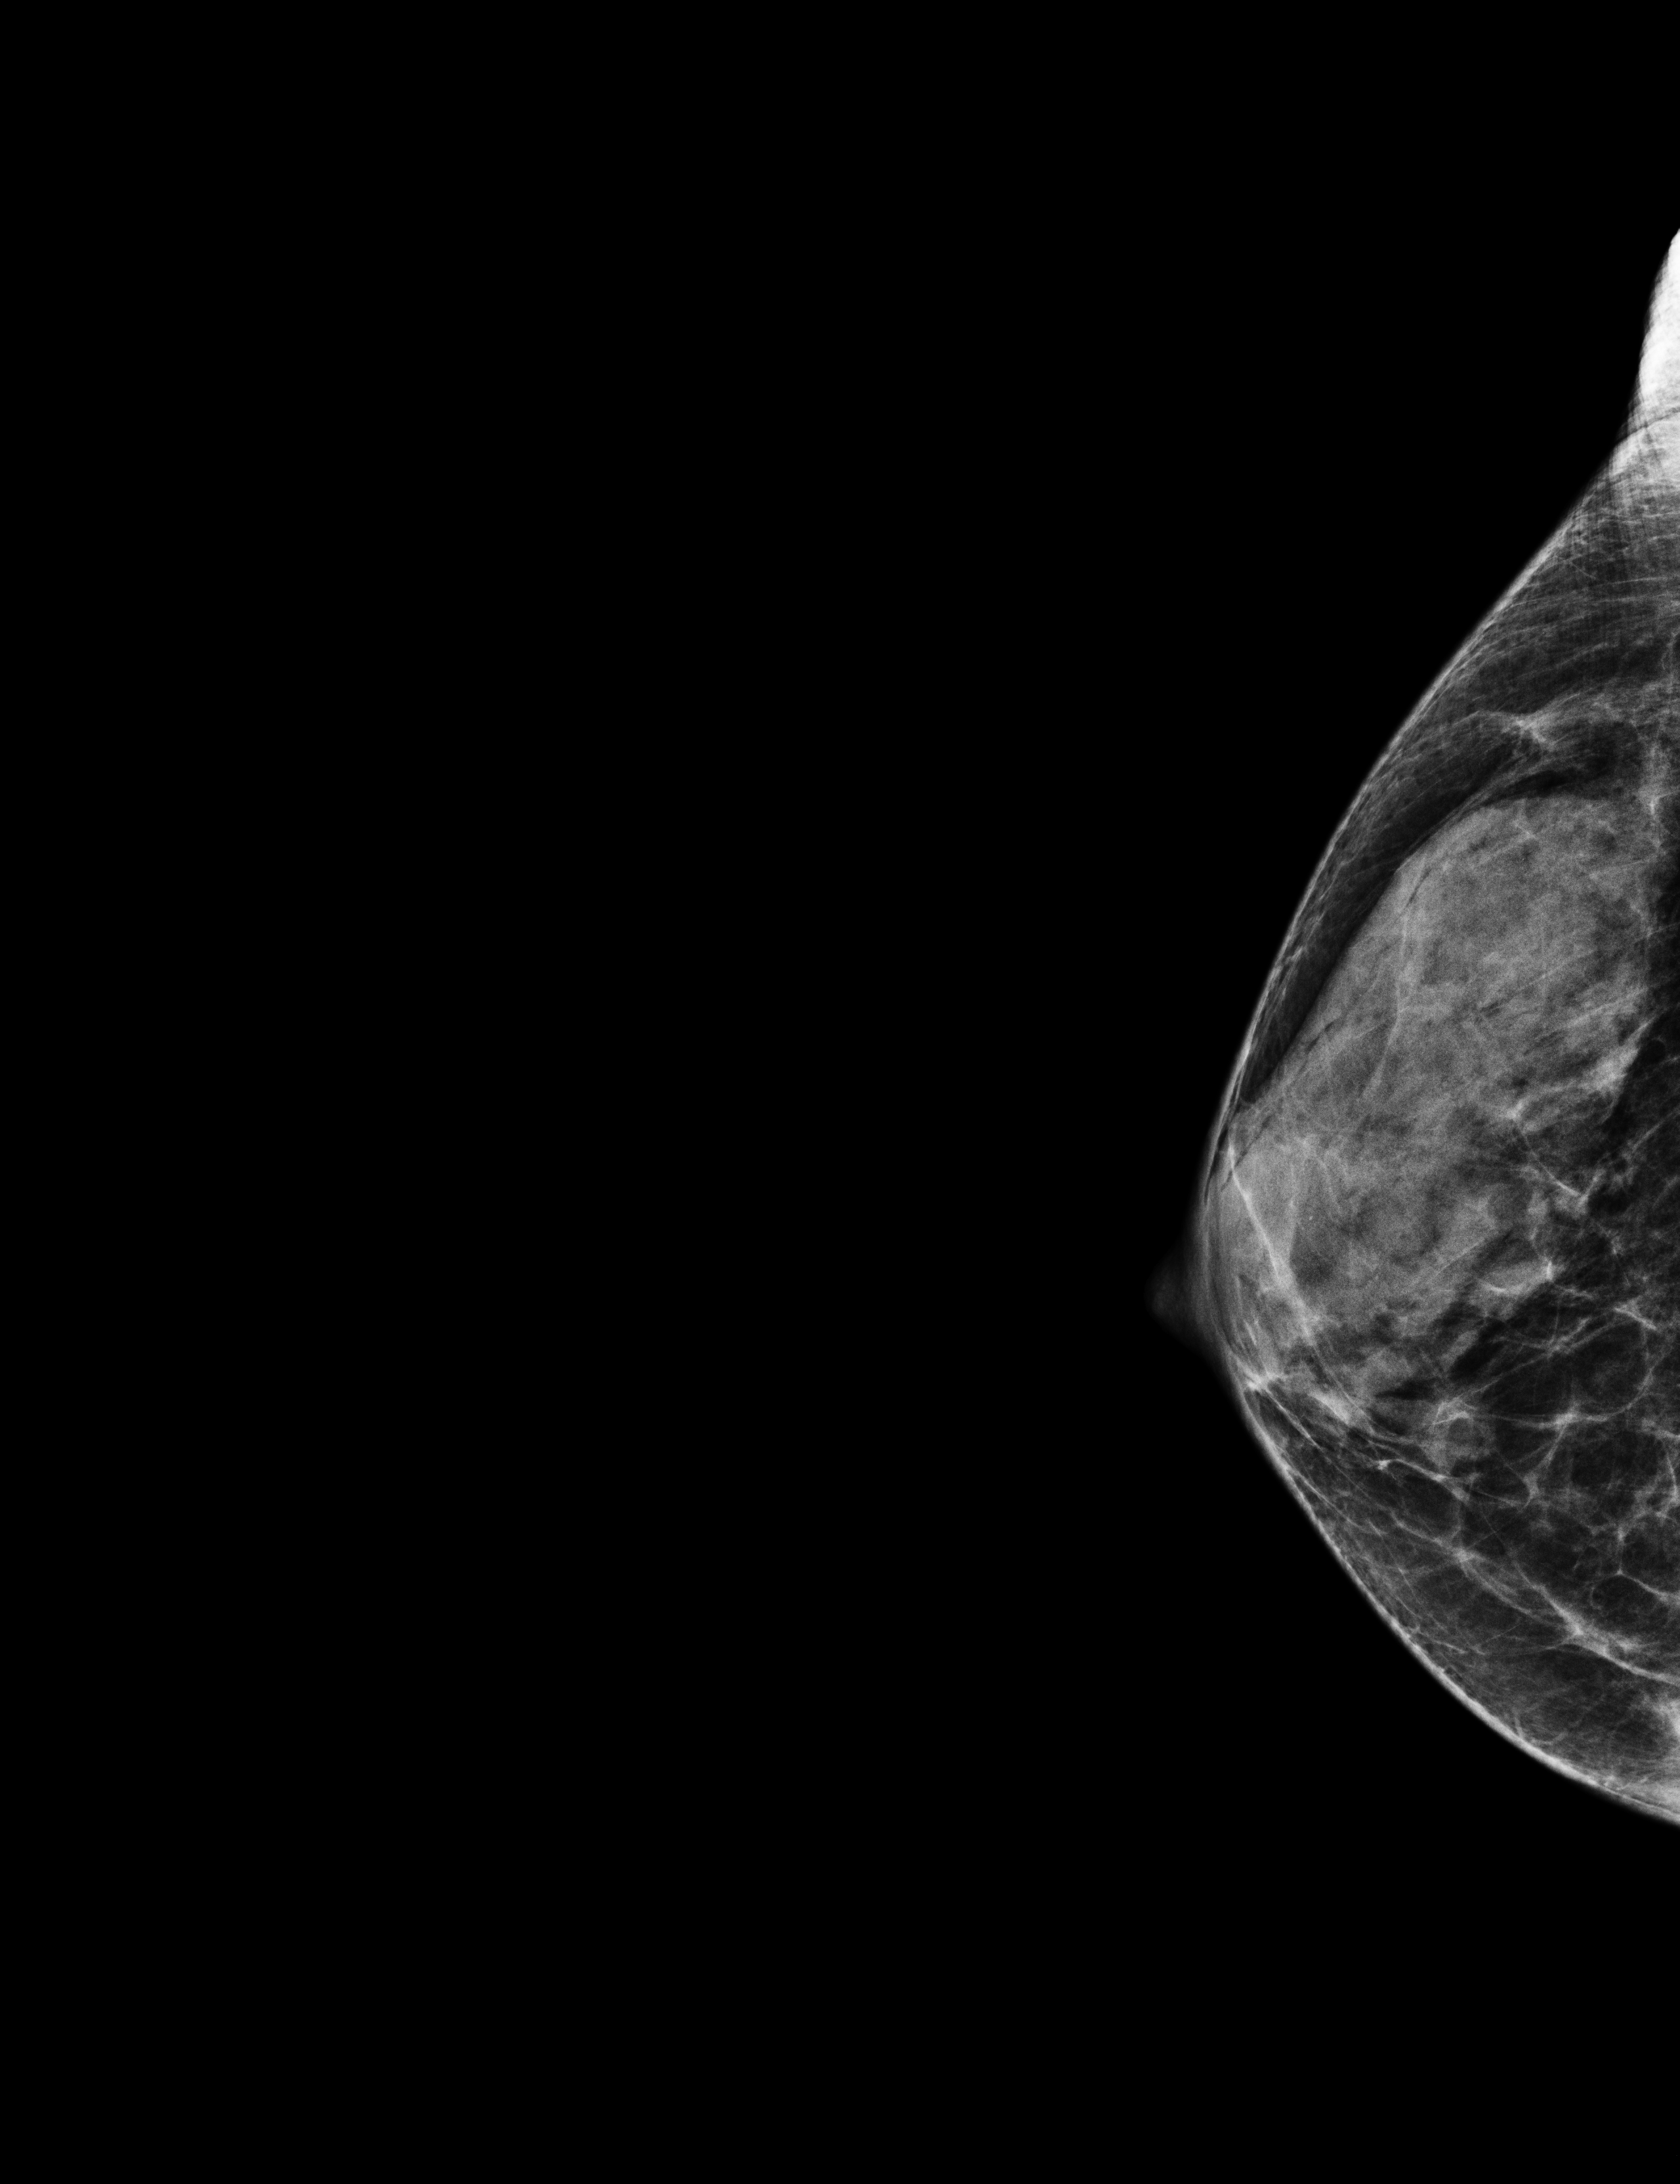
Annual screening mammography examination, compressed breast thickness 30 mm, system: Selenia Dimensions. Female patient, age 61 years.
Image type: full-field digital mammogram. Breast: right. Projection: exaggerated CC view (lateral).